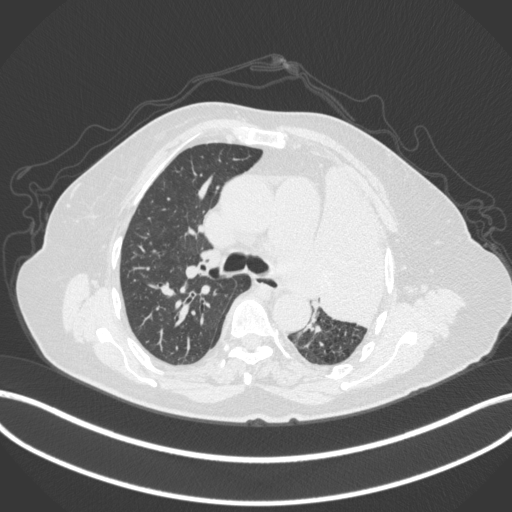
Chest CT, one axial slice; position 253 of 399 along the scan axis; reconstruction kernel B31f; lung window (W 1500 / L -600 HU); 512 × 512 image matrix. Female patient, age 75 years. From the clinical record (not read from this slice): clinical TNM (as recorded): T3 N3 M1.
Annotated regions visible in this slice (rectangle marked by the reading radiologist):
- lung tumour (recorded histology: adenocarcinoma): bounding box <316,161,401,332> (left, top, right, bottom; pixels)